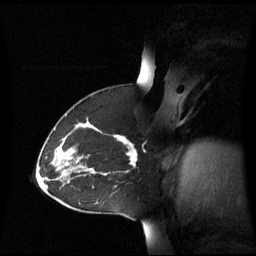
Breast MRI (dynamic contrast-enhanced), one sagittal slice; slice 39 of 60 in the series (ordered by position); dynamic contrast-enhanced series, image 2 of 3 at this slice position (ordered by acquisition); 1.5 T; TE 4.2 ms, TR 8.4 ms; 2.8 mm slice thickness; 256 × 256 image matrix, field of view 270 × 270 mm. Female patient, age 43 years. Case-level facts recorded for this patient, not image findings: setting: breast cancer imaged before/during neoadjuvant chemotherapy; receptor status: triple-negative.
Outlined on this slice (semi-automatically segmented with operator editing):
- analysis volume of interest (the breast-tissue region the enhancement analysis was run in; not a lesion): bounding box (x1, y1, x2, y2) in pixels: (55, 124, 138, 173)
- tumour enhancement mask (voxels above the 70 % enhancement threshold inside the analysis volume of interest): (71, 137, 137, 166)